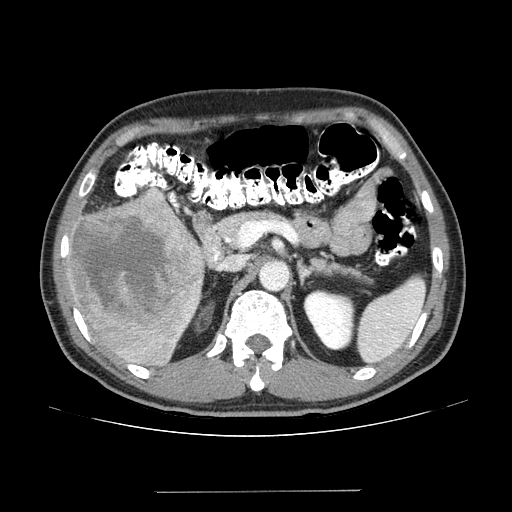
Contrast-enhanced abdominal CT (liver protocol), one axial slice. Slice 75 of 131 in the series (ordered by position). Reconstruction kernel STANDARD. One of 2 acquisitions stored at this slice position. Soft-tissue window (W 400 / L 40 HU). 2.5 mm slice thickness. 512 × 512 image matrix. From the clinical record (not read from this slice): diagnosis: hepatocellular carcinoma (patient treated with transarterial chemoembolisation; whether this scan precedes or follows treatment is not stated here); TNM stage (as recorded): Stage-I; Child-Pugh class: A; tumour nodularity: uninodular.
Annotated regions visible in this slice (semi-automatic segmentation, software-assisted and operator-edited):
- liver parenchyma outside the tumour (the mass and vessels are separate outlines, so this box may not span the whole liver): bounding box (x1, y1, x2, y2) in pixels: (64, 188, 204, 366)
- mass: (71, 192, 202, 328)